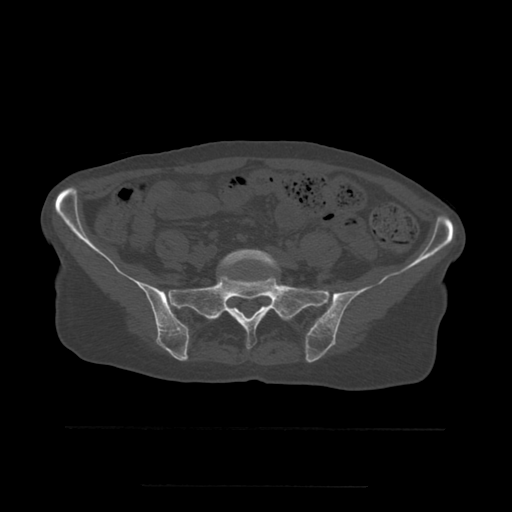
CT including the spine, one axial slice; position 131 of 544 along the scan axis; bone window (W 1800 / L 400 HU); 1.25 mm slice thickness; 512 × 512 image matrix, field of view 350 × 350 mm. Patient age 58 years. From the clinical record (not read from this slice): primary cancer: lung.
Structures marked on this image (semi-automatic segmentation, software-assisted and operator-edited):
- L5 vertebra: bounding box [x1, y1, x2, y2] px = [219, 249, 280, 271]